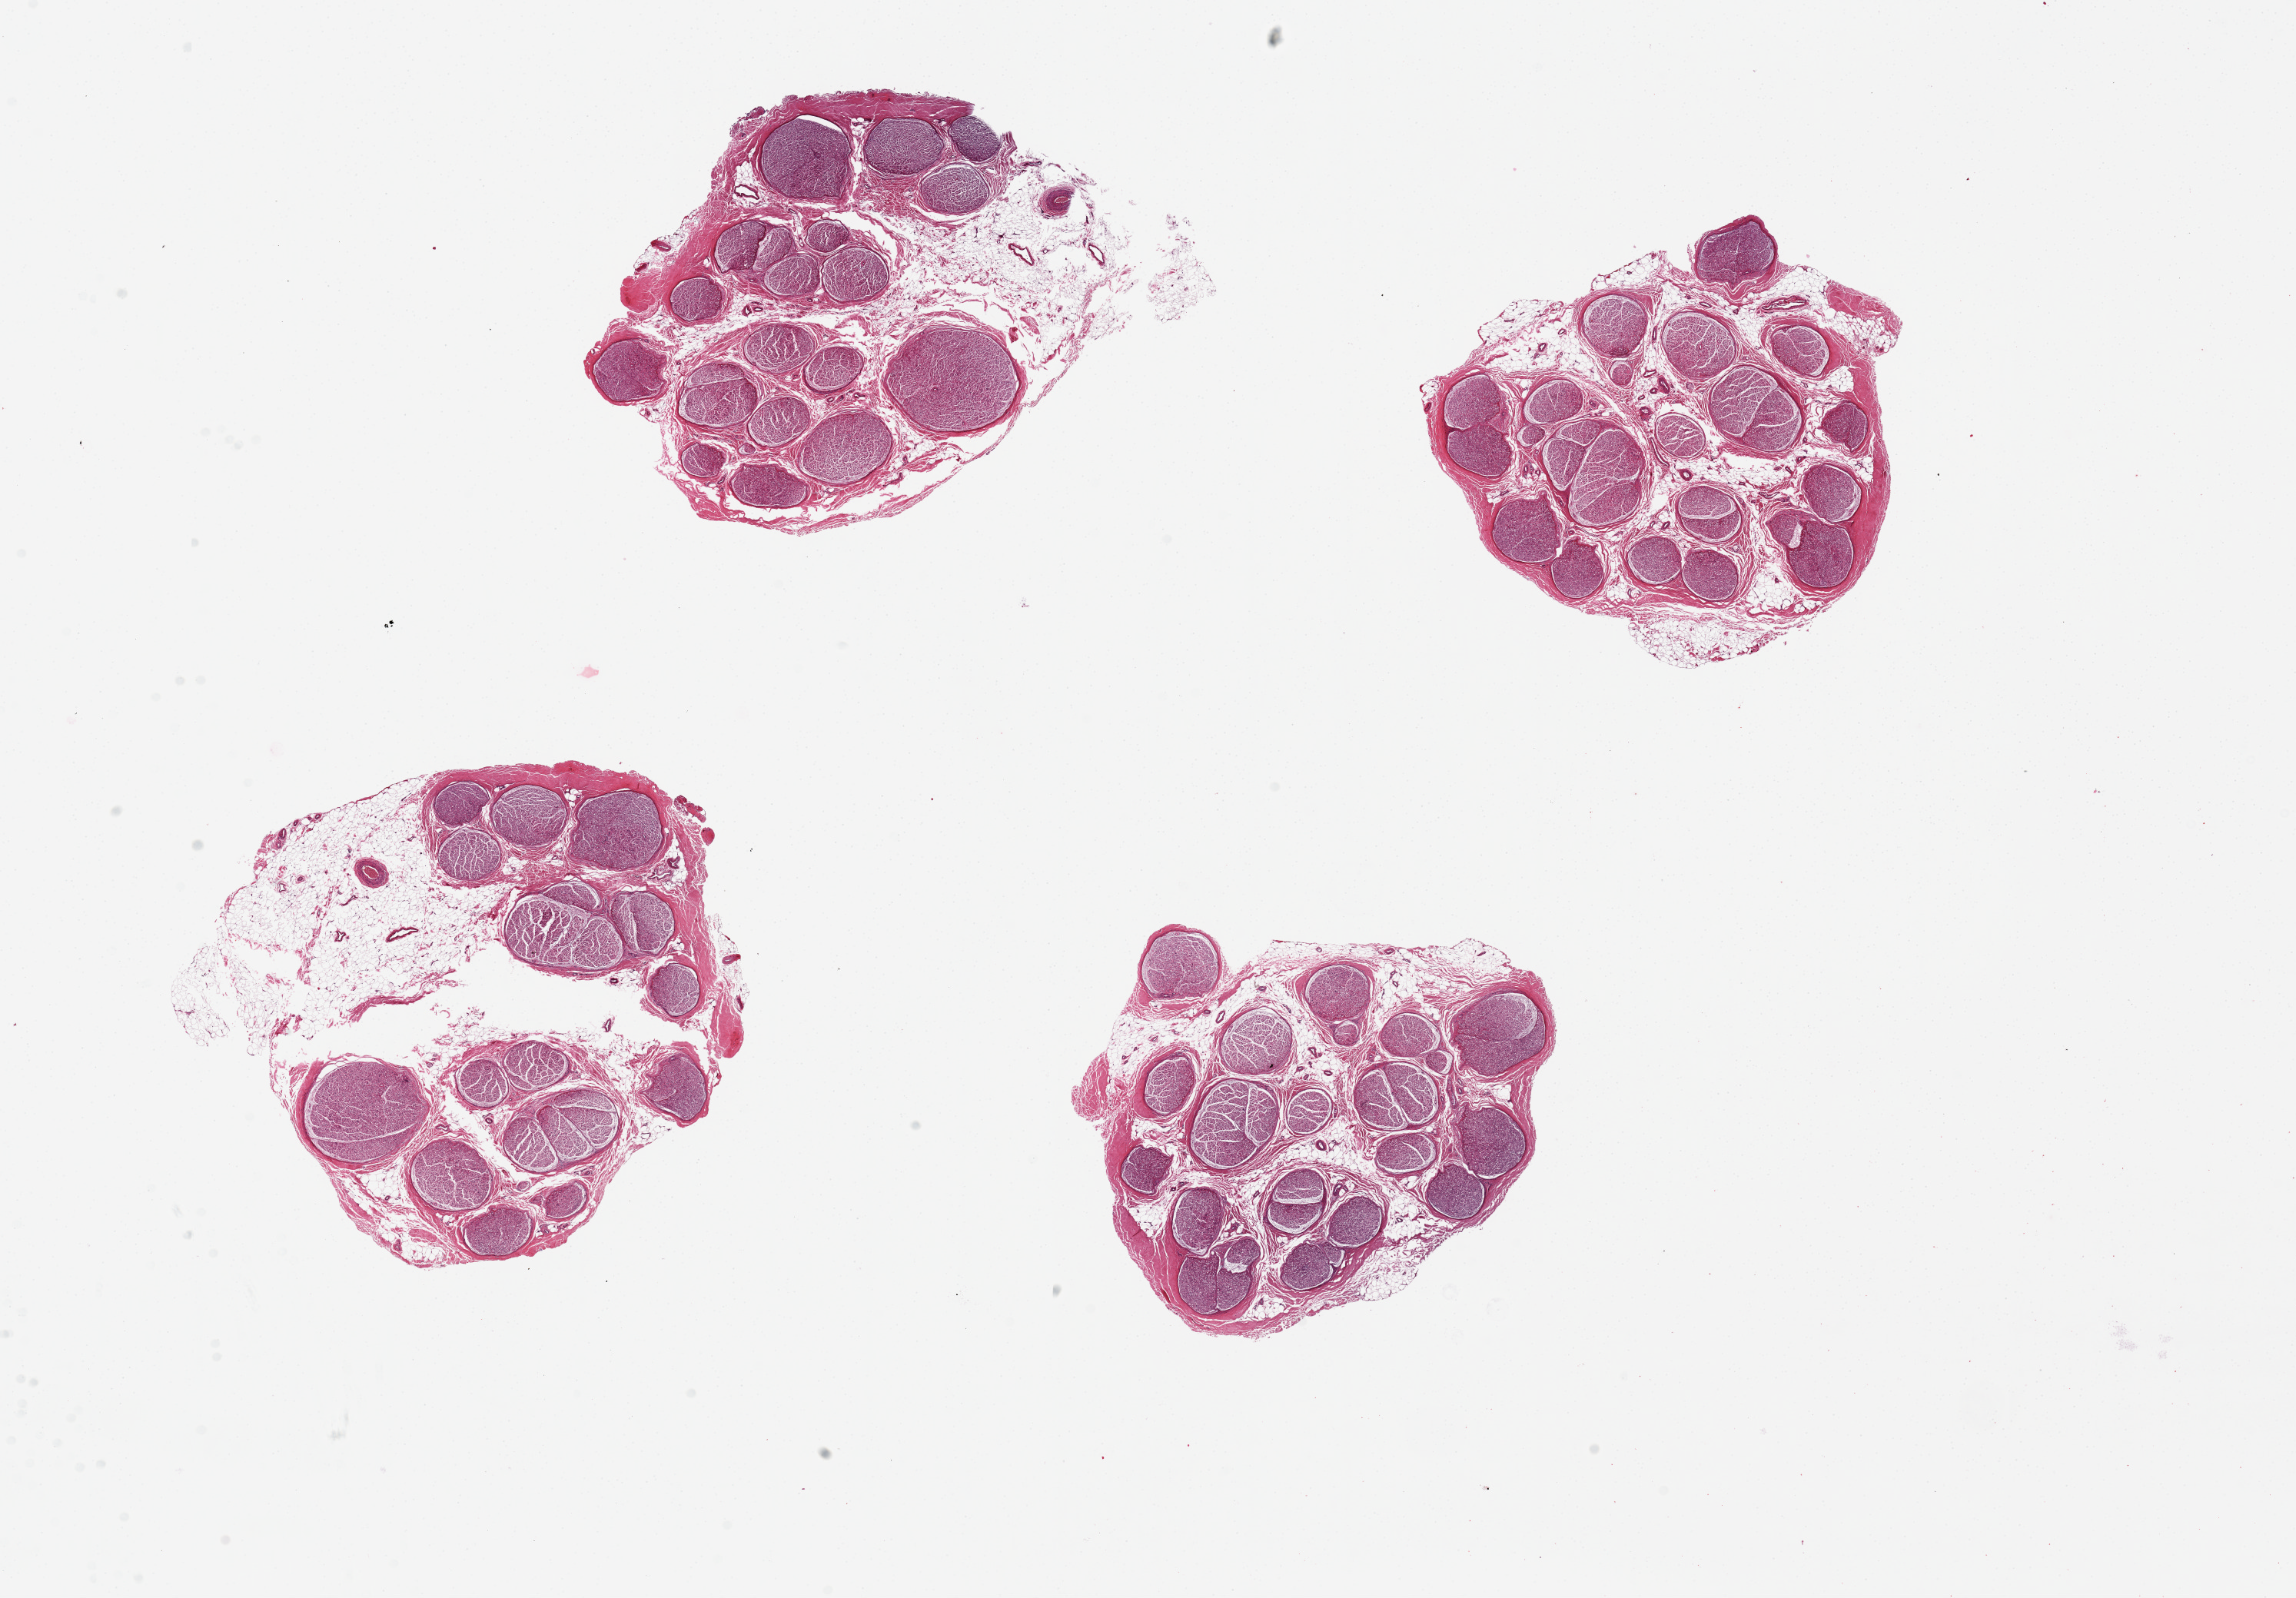
H&E whole-slide image, a low-resolution overview of the entire scanned area, about 23.6 x 16.4 mm, PAXgene-fixed paraffin-embedded (PFPE) section, target tissue: tibial nerve, donor tissue sample. Donor sex: male.
Reviewer comment on this tissue sample: 4 pieces, from 4.5x4 to 5x5mm; 40% intyernsal and external fat.